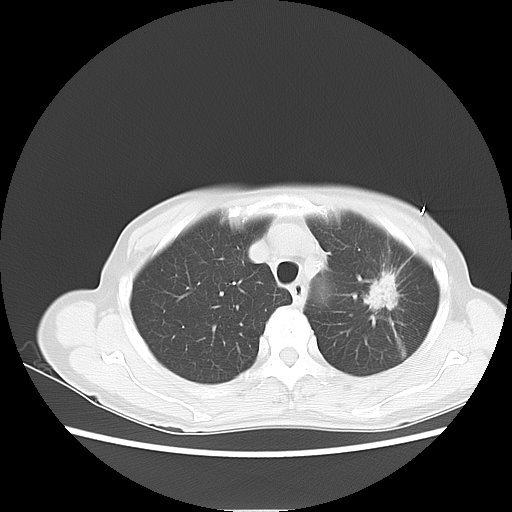
Chest CT, one axial slice; slice 8 of 14 in the series (ordered by position); reconstruction kernel LUNG; 120 kVp; lung window (W 1500 / L -600 HU); 512 × 512 image matrix, field of view 350 × 350 mm. Female patient, age 71 years. Case-level facts recorded for this patient, not image findings: clinical TNM (as recorded): T2 N0 M0.
Outlined on this slice (rectangle marked by the reading radiologist):
- lung tumour (recorded histology: adenocarcinoma): bounding box [x1, y1, x2, y2] px = [362, 265, 404, 314]